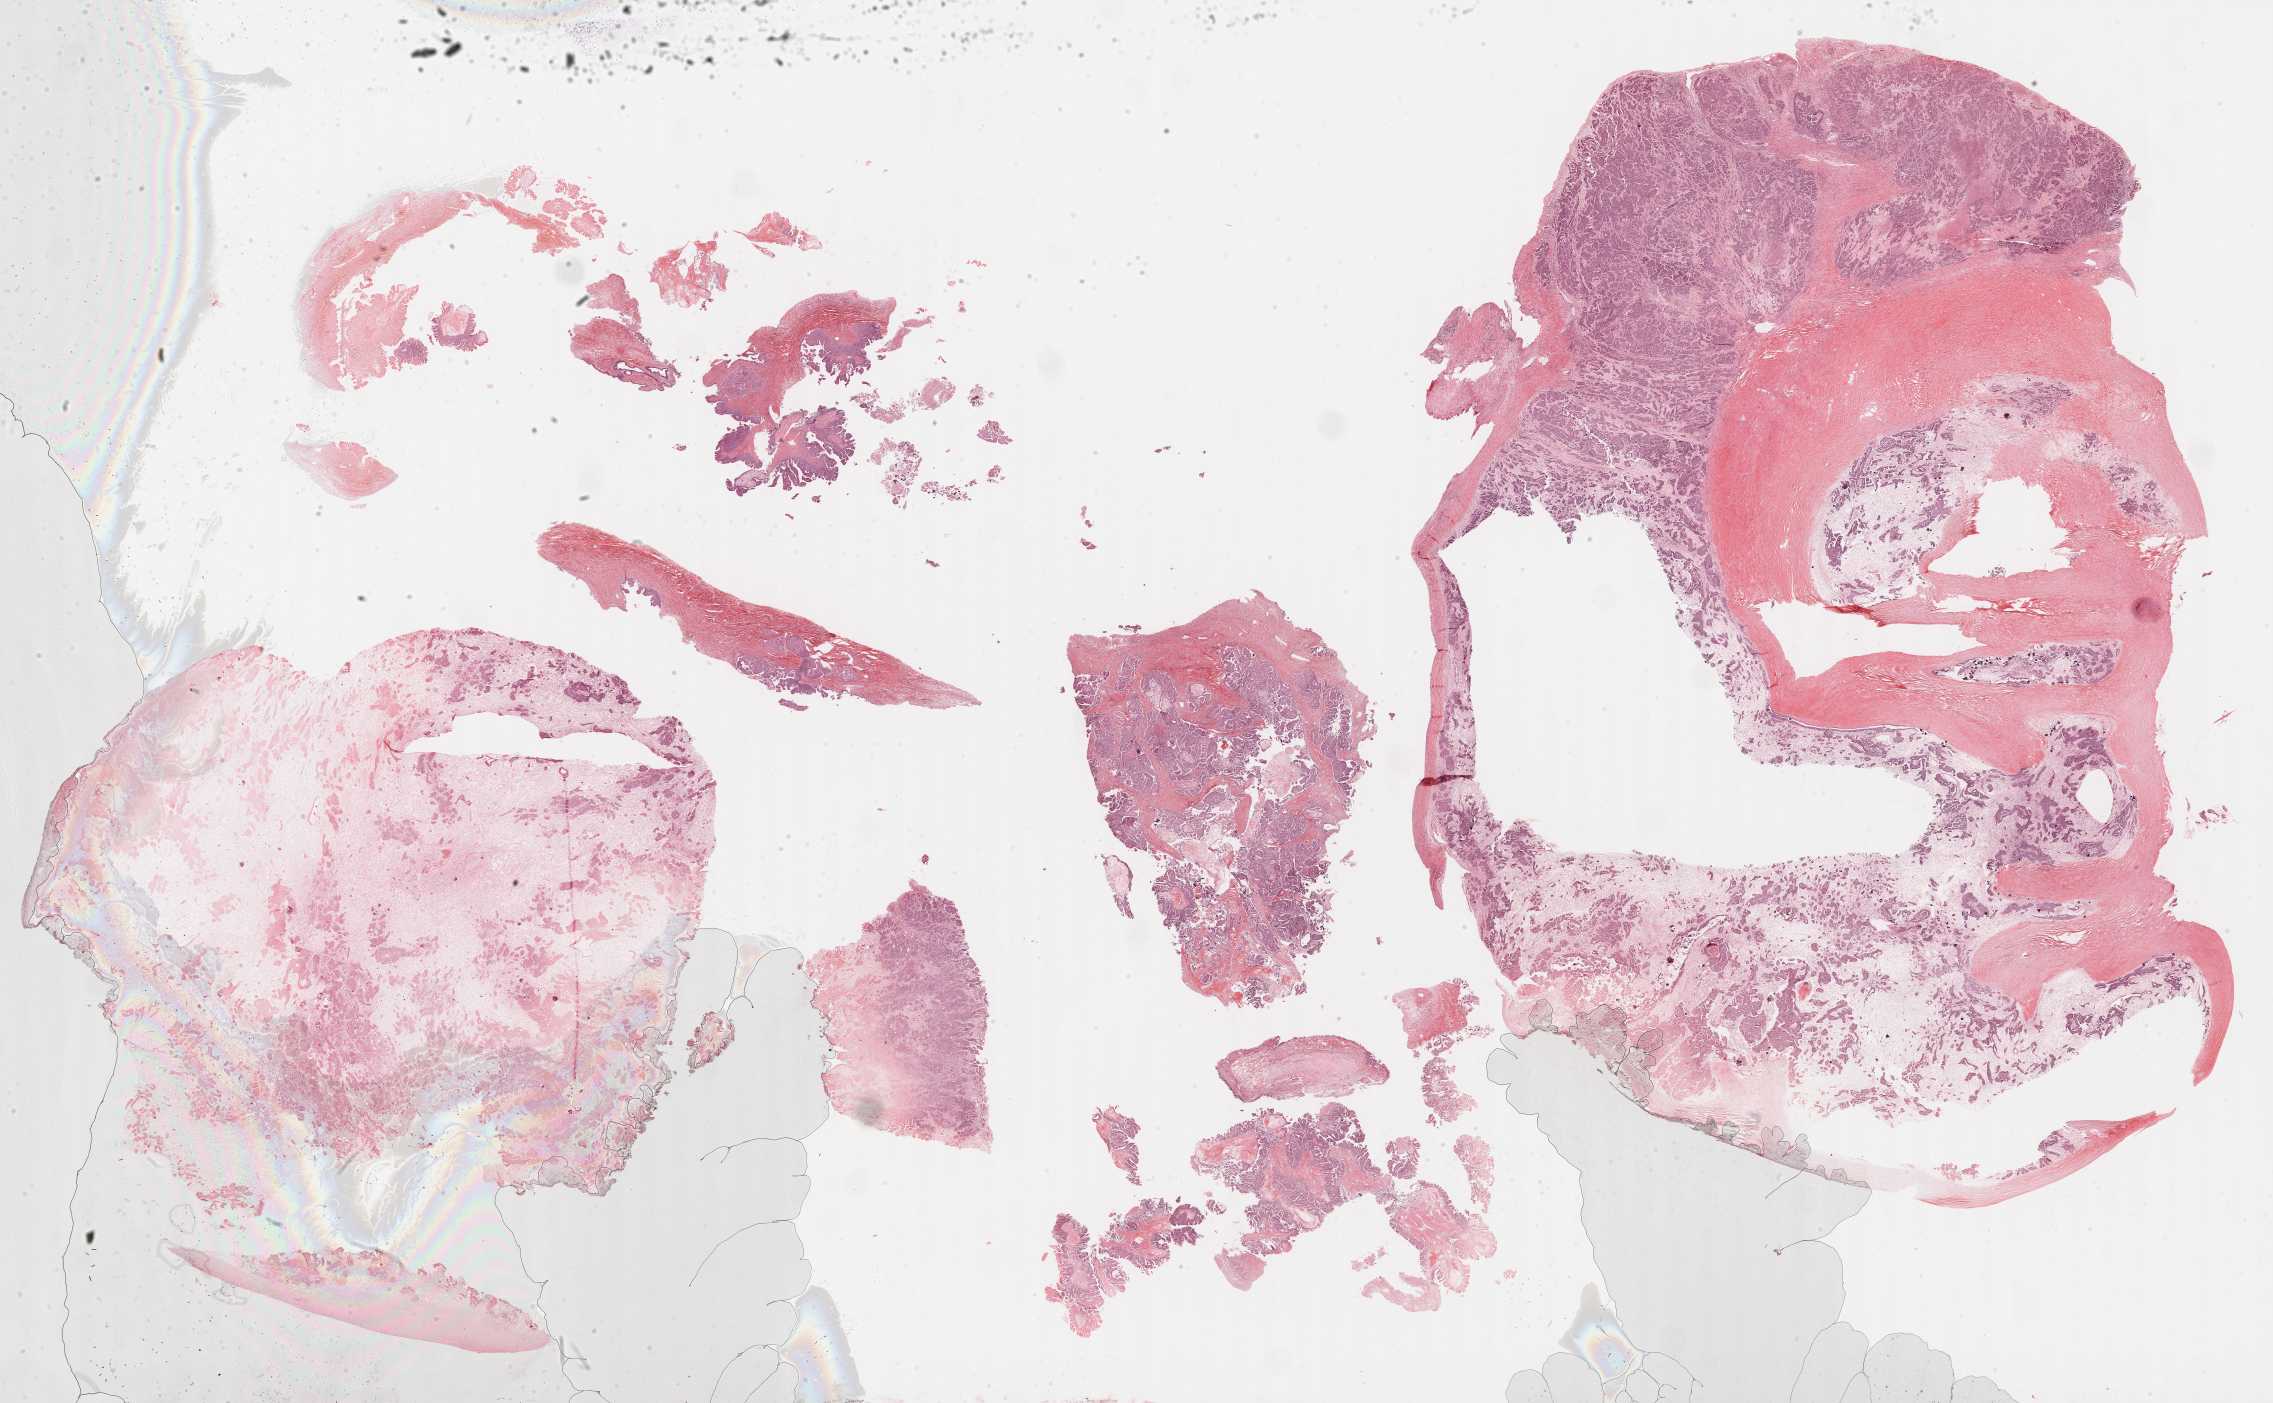
Digitized H&E tissue section (whole slide), whole scanned area (about 36.7 x 22.7 mm) shown as a low-resolution overview; FFPE section; primary tumour sample from the ovary. Female patient; age at initial diagnosis 66 years. Histologic grade: G3 (poorly differentiated).
FIGO stage: IIIC. Diagnosis: Serous cystadenocarcinoma, NOS.